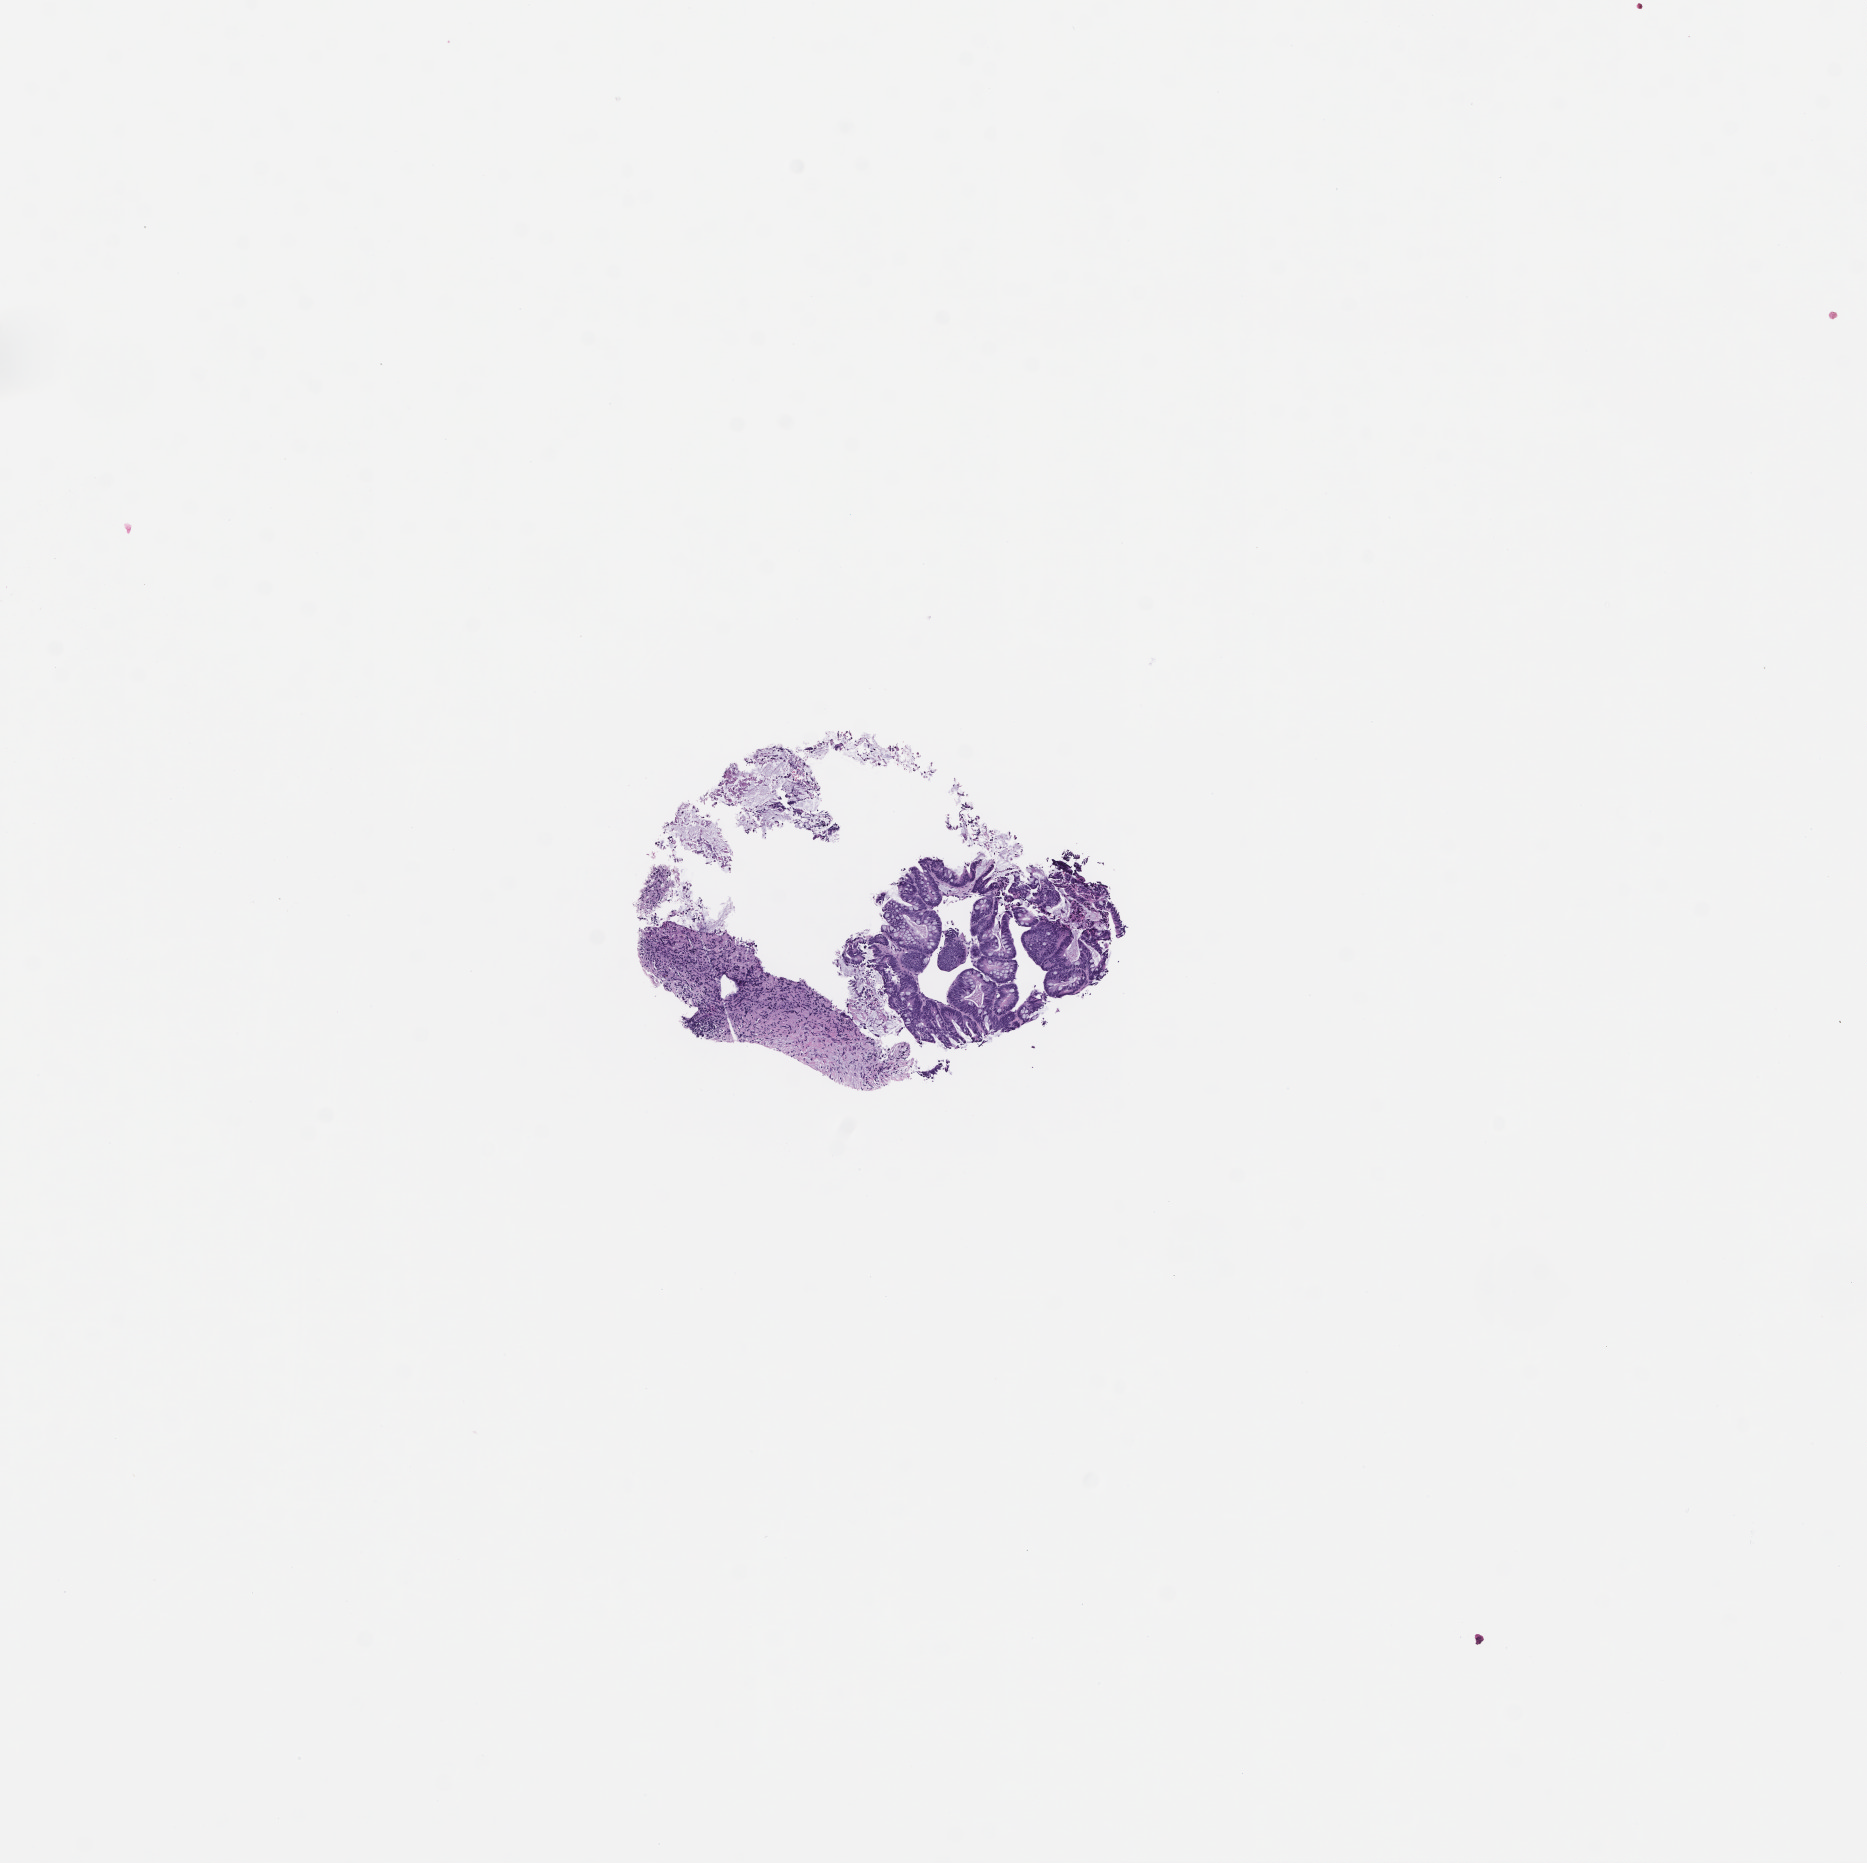
H&E whole-slide image — whole scanned area (about 7.5 x 7.5 mm) shown as a low-resolution overview. Formalin-fixed paraffin-embedded section. Patient sex: female.
* this section: metastatic tumor tissue
* patient diagnosis (primary): Colorectal Carcinoma